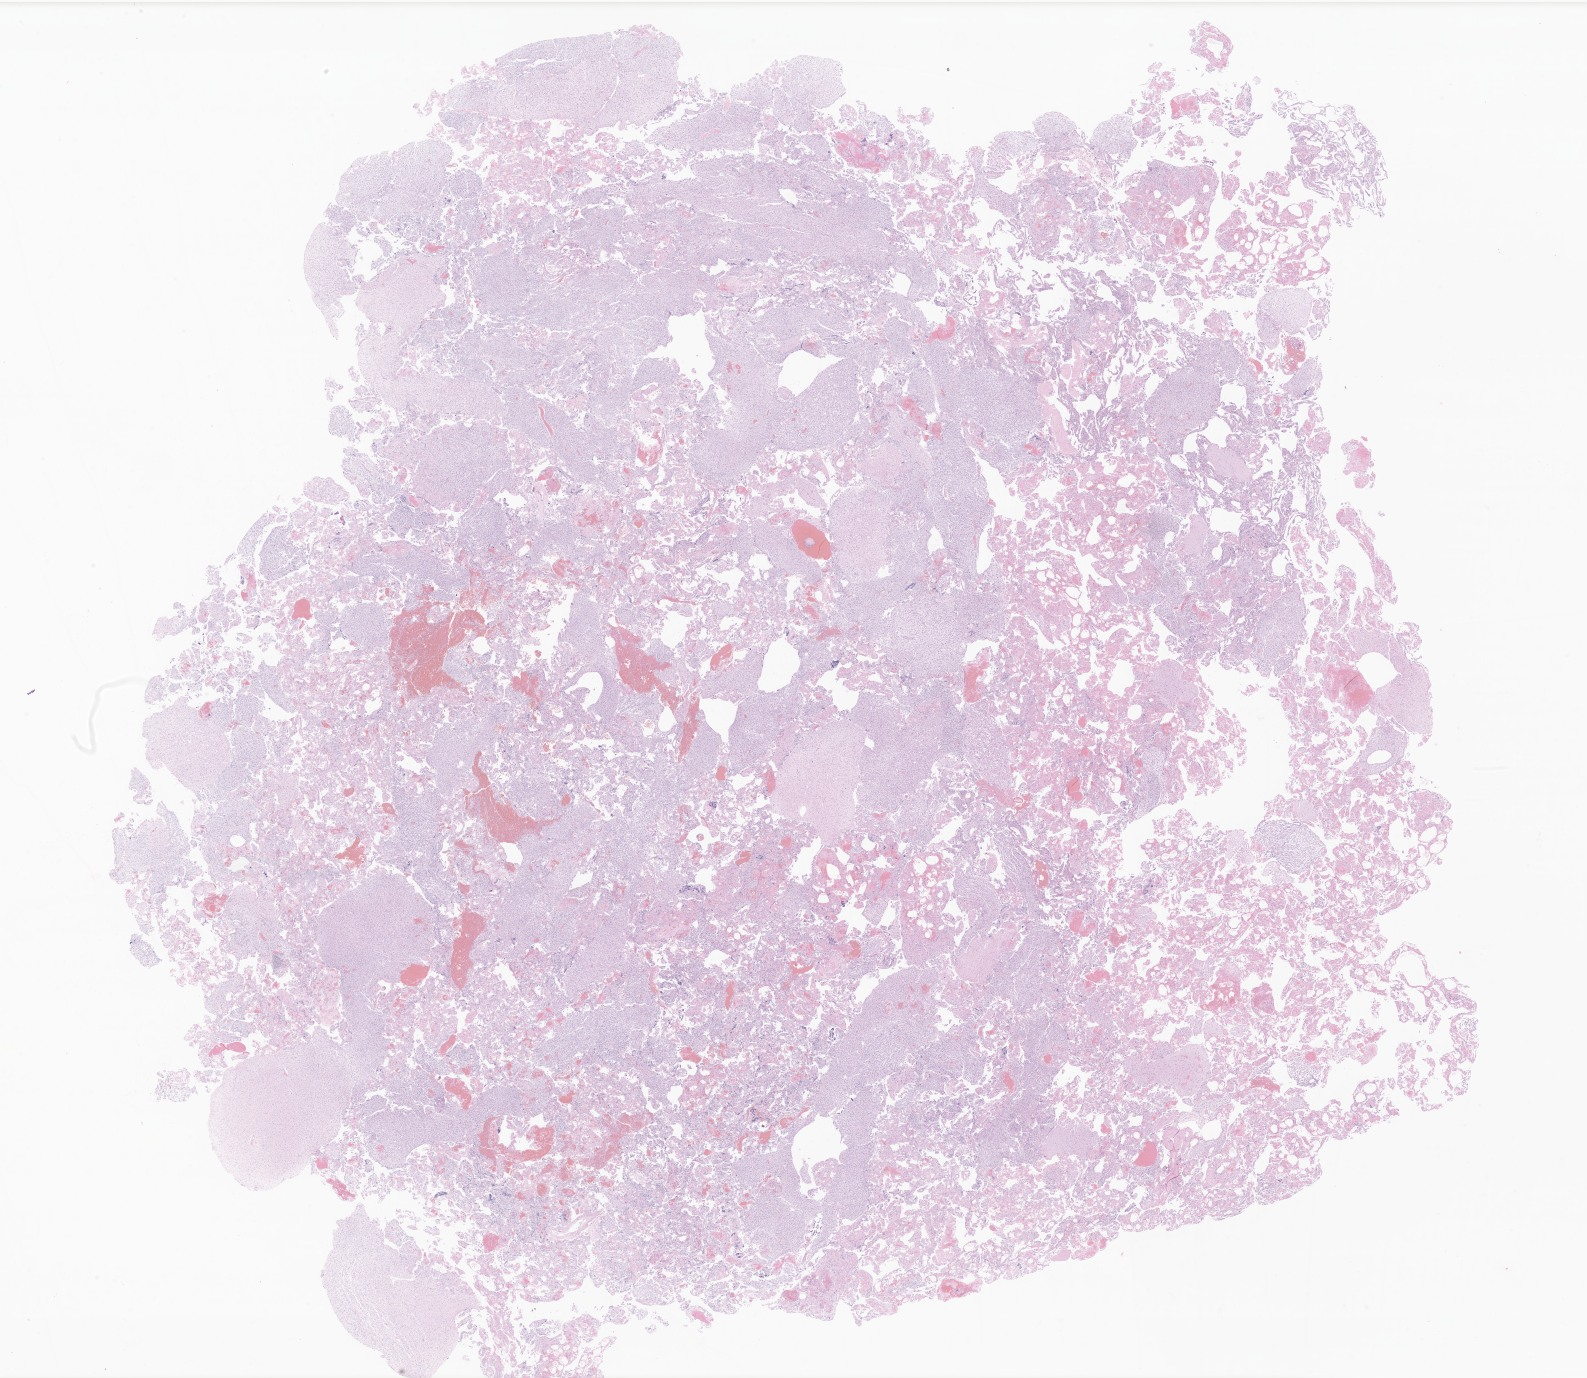
Haematoxylin and eosin whole-slide image of tumor tissue from the brain, whole scanned area (about 26.8 x 23.2 mm) shown as a low-resolution overview. Formalin-fixed, paraffin-embedded (FFPE) tissue. Patient male; age 197 months (16 years 5 months).
Recorded diagnosis: Astrocytoma, NOS.